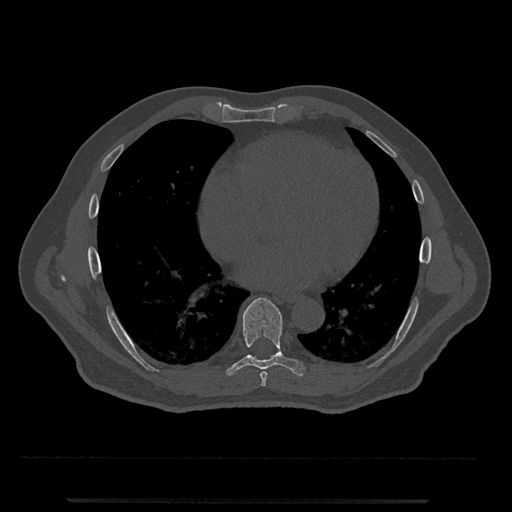
CT including the spine, one axial slice. Slice 631 of 797 in the series (ordered by position). Reconstruction kernel Br40s/3. 120 kVp. Bone window (W 1800 / L 400 HU). 512 × 512 image matrix, field of view 419 × 419 mm. Patient: male, 63 years. Case-level facts recorded for this patient, not image findings: primary cancer: prostate.
Structures marked on this image (semi-automatically segmented with operator editing):
- T7 vertebra: bounding box (x1, y1, x2, y2) in pixels: (260, 371, 268, 387)
- T8 vertebra: (225, 298, 306, 377)